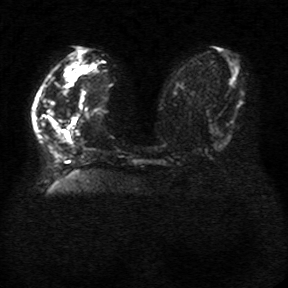
Breast MRI, one axial slice. Slice 13 of 34 in the series (ordered by position). Diffusion-weighted series; image 2 of 4 stored at this slice position (different b-values; order by instance number). 1.5 T. 5 mm slice thickness. 288 × 288 image matrix, field of view 340 × 340 mm. Female patient.
Outlined on this slice (manually delineated by an expert):
- tumour on diffusion-weighted imaging: bounding box [x1, y1, x2, y2] px = [46, 99, 58, 126]